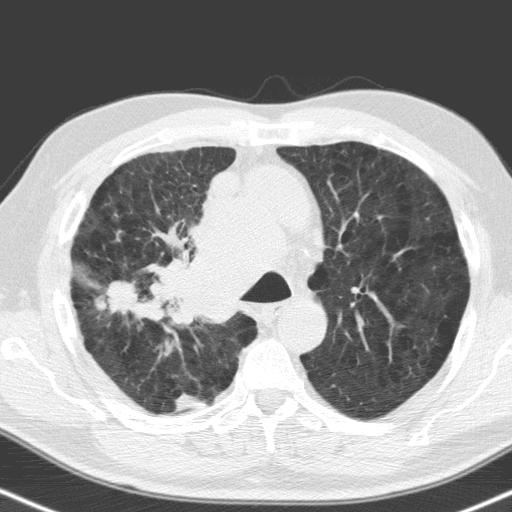
Low-dose screening chest CT, one axial slice. 120 kVp. Lung window (W 1500 / L -600 HU). 3.2 mm slice thickness. 512 × 512 image matrix, field of view 324 × 324 mm.
Annotated regions visible in this slice (manually delineated by an expert):
- lesion 1 (tumor, hilum of right lung): bounding box (x1, y1, x2, y2) in pixels: (162, 200, 264, 322)
- lesion 2 (tumor, upper lobe of right lung): (108, 281, 146, 317)